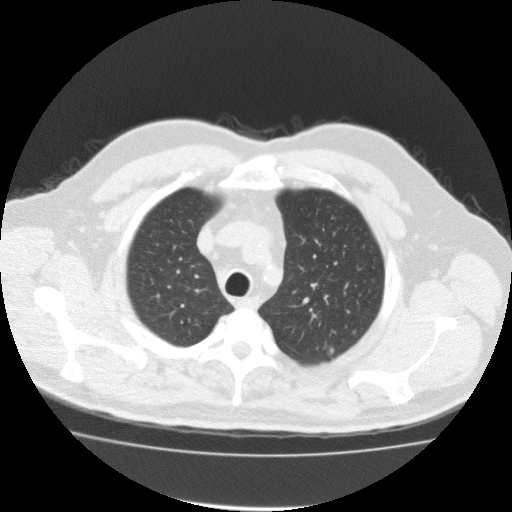
Low-dose screening chest CT, one axial slice; slice 137 of 161 in the series (ordered by position); 120 kVp; lung window (W 1500 / L -600 HU); 2 mm slice thickness; 512 × 512 image matrix, field of view 412 × 412 mm.
Annotated regions visible in this slice (expert manual segmentation):
- lesion 1 (tumor, upper lobe of left lung): bounding box <328,347,334,355> (left, top, right, bottom; pixels)